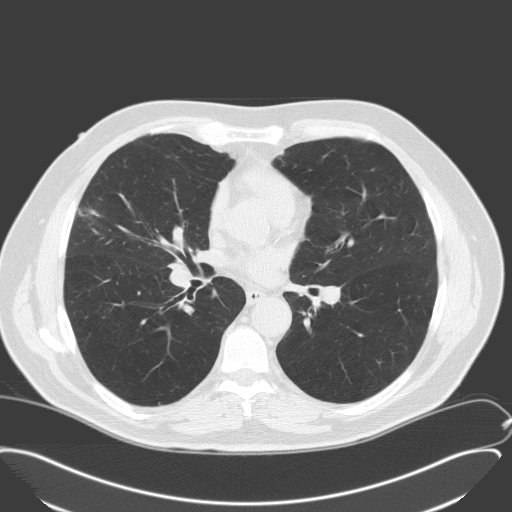
Chest CT (low-dose screening protocol), one axial image. Second screening round (one year after baseline). Lung window (W 1500 / L -600 HU). 3.2 mm slice thickness. Standard (soft-tissue) reconstruction kernel (C). Slice 84 of 175 in the series. Male, age 65 years at enrolment. Former smoker at enrolment.
Expert reader's lesion annotation, bounding box [x1, y1, x2, y2] px = [62, 193, 115, 245]. Screening reader's record for this exam: no non-calcified nodule ≥4 mm recorded. Official screen result: negative screen, minor abnormalities not suspicious for lung cancer. Later outcome: lung cancer diagnosed 346 days after this screen — adenocarcinoma, NOS, right middle lobe, moderately differentiated (G2), stage IA (AJCC 6th edition), 25 mm at pathology.